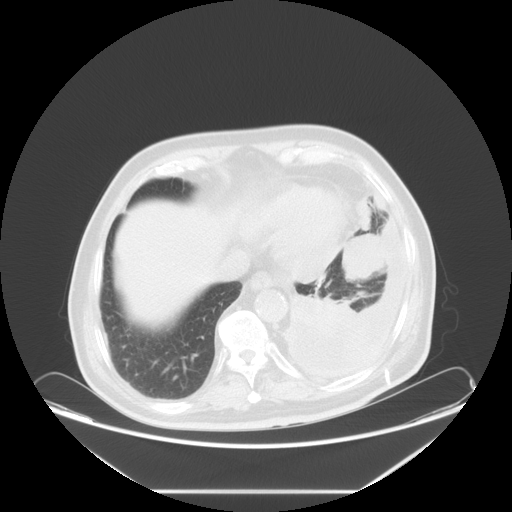
Chest CT, one axial slice. Slice 18 of 63 in the series (ordered by position). Reconstruction kernel STANDARD. Lung window (W 1500 / L -600 HU). 512 × 512 image matrix, field of view 448 × 448 mm. Patient: male, 67 years. From the clinical record (not read from this slice): clinical TNM (as recorded): T1b N1 M1a; histopathological grade: G3.
Outlined on this slice (bounding box drawn by a radiologist):
- lung tumour (recorded histology: small cell carcinoma): box from (x=337, y=225) to (x=390, y=287) px